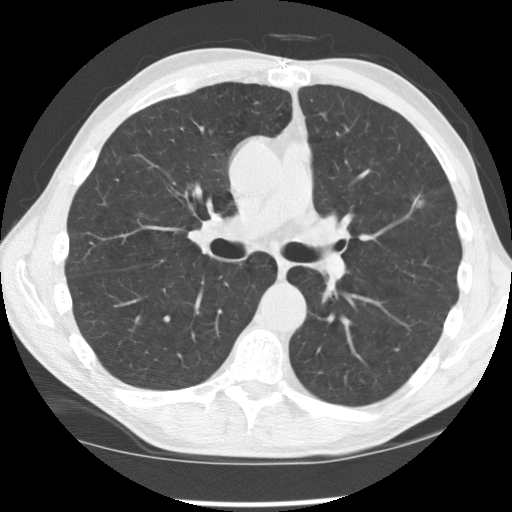
Low-dose screening chest CT, one axial slice; 120 kVp; lung window (W 1500 / L -600 HU); 2.5 mm slice thickness; 512 × 512 image matrix.
Structures marked on this image (manually delineated by an expert):
- lesion 1 (tumor, upper lobe of left lung): bounding box (x1, y1, x2, y2) in pixels: (417, 201, 423, 207)